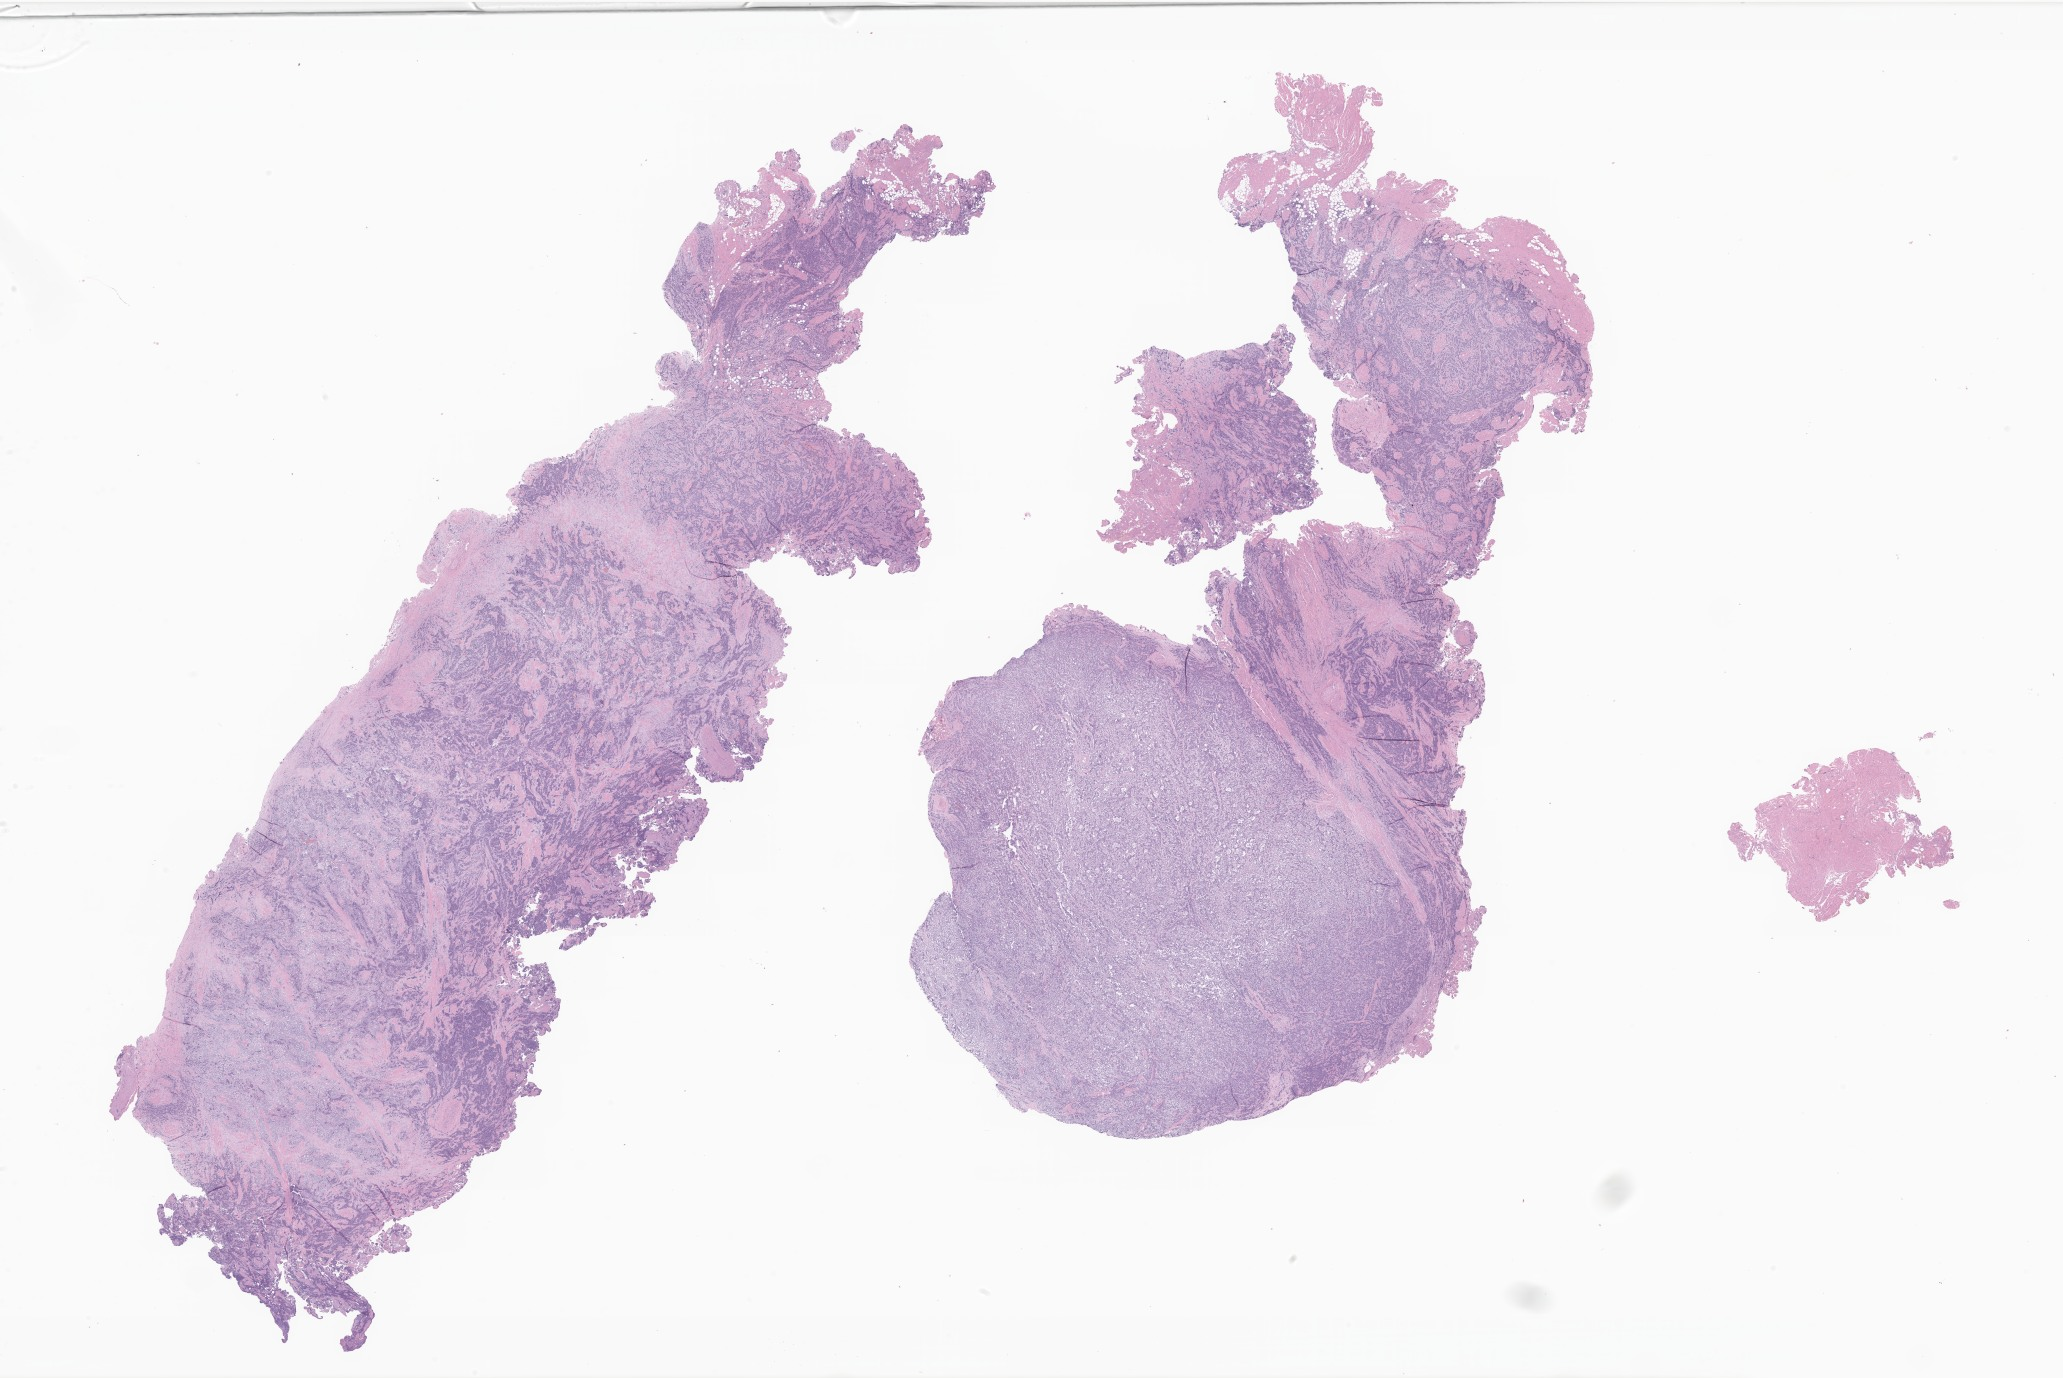
Whole-slide image, H&E stain of tumor tissue from the lip, shown as a low-resolution overview of the whole scanned area (about 34.8 x 23.2 mm), FFPE section. Patient: female, age 54 months (4 years 6 months).
Diagnosis (ICD-O-3 morphology term): Alveolar rhabdomyosarcoma.